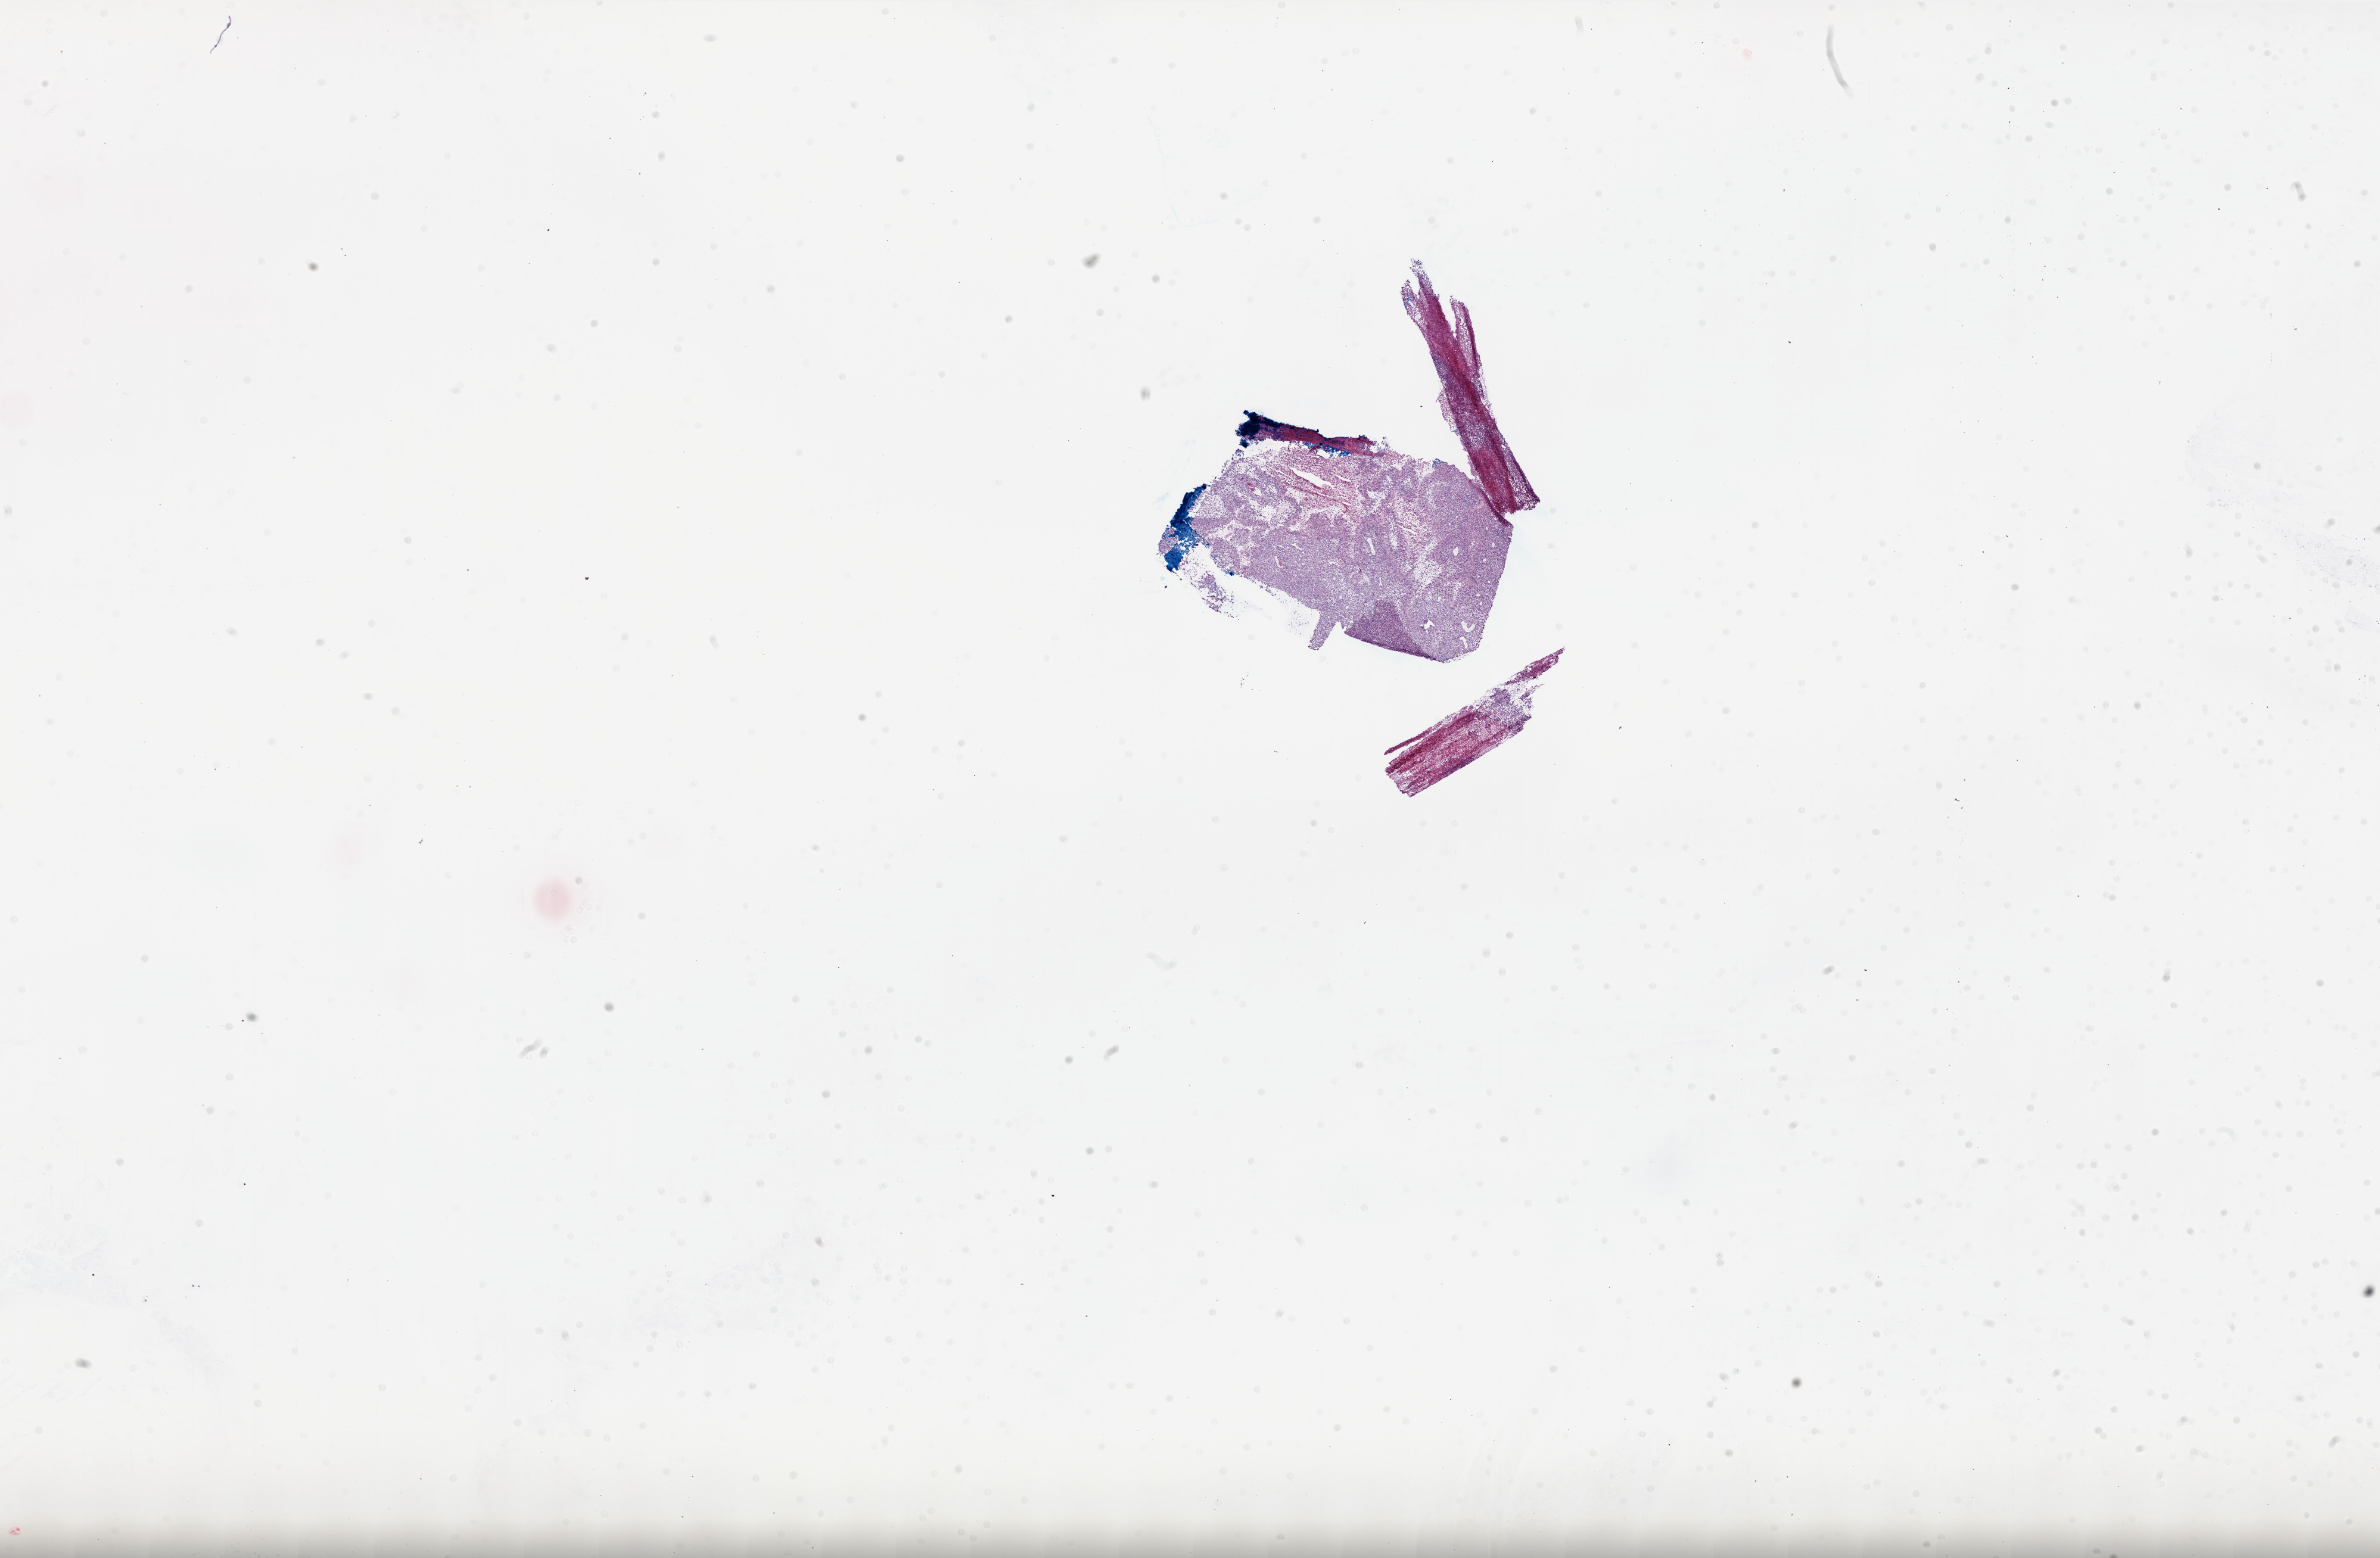
Digitized H&E tissue section (whole slide), shown as a low-resolution overview of the whole scanned area (about 32.0 x 20.9 mm, acquisition: 20x scan), frozen section, primary tumour sample from the brain. Patient: female, age at initial diagnosis 57 years. Composition of this section per pathologist review: tumour cells 80%, tumour nuclei 90%, normal cells 0%, stromal cells 15%, necrosis 5%.
• histologic diagnosis: Glioblastoma